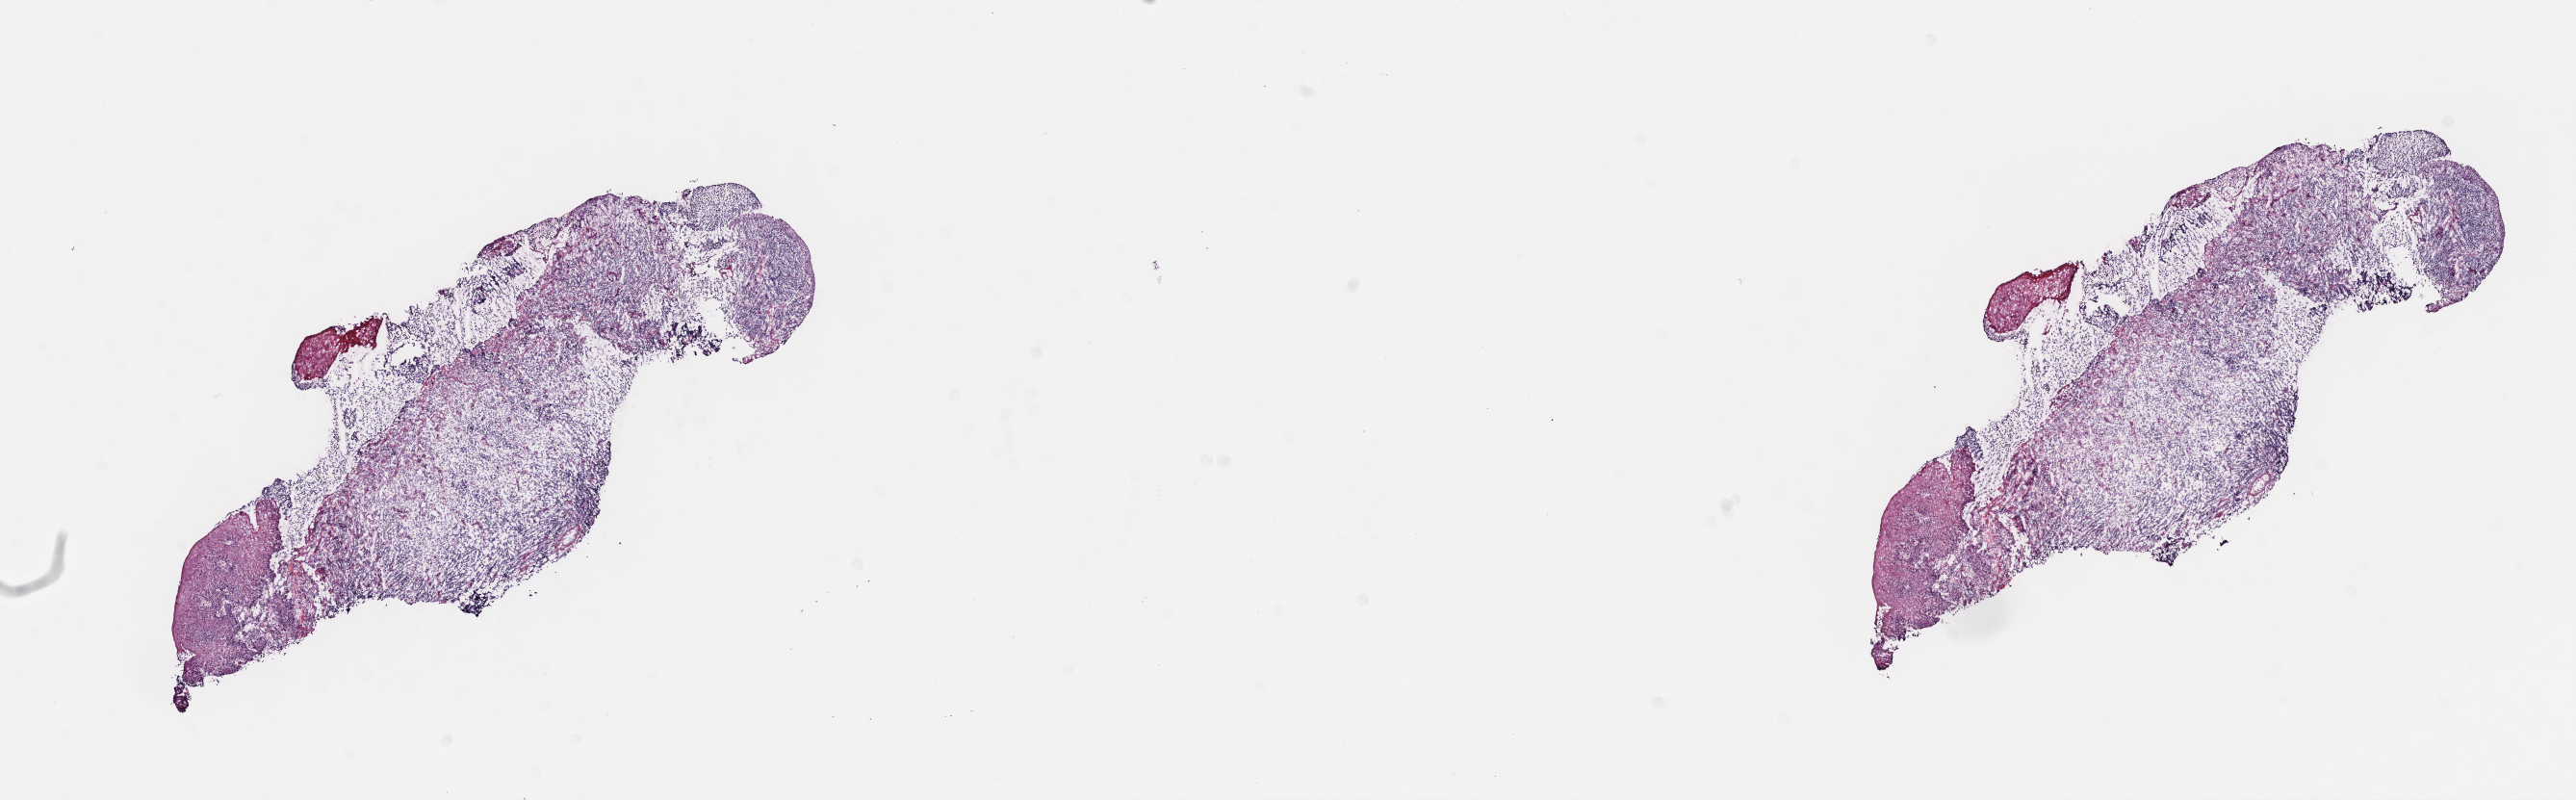
Digitized hematoxylin and eosin (H&E)-stained section, shown as a low-resolution overview of the whole scanned area (about 21.6 x 6.7 mm); frozen section (tissue freezing medium); primary tumor; anatomic site: mandible. Male patient; age at initial diagnosis 5 years. Composition of this section per pathologist review: tumor cells 90%, tumor nuclei 90%, stromal cells 10%, necrosis 0%, normal cells 0%. Infiltration values recorded for this section: lymphocyte infiltration 3%, monocyte infiltration 5%, neutrophil infiltration 0%.
• section: top of the tissue portion
• Ann Arbor stage (patient): Stage I
• diagnosis: Burkitt lymphoma, NOS